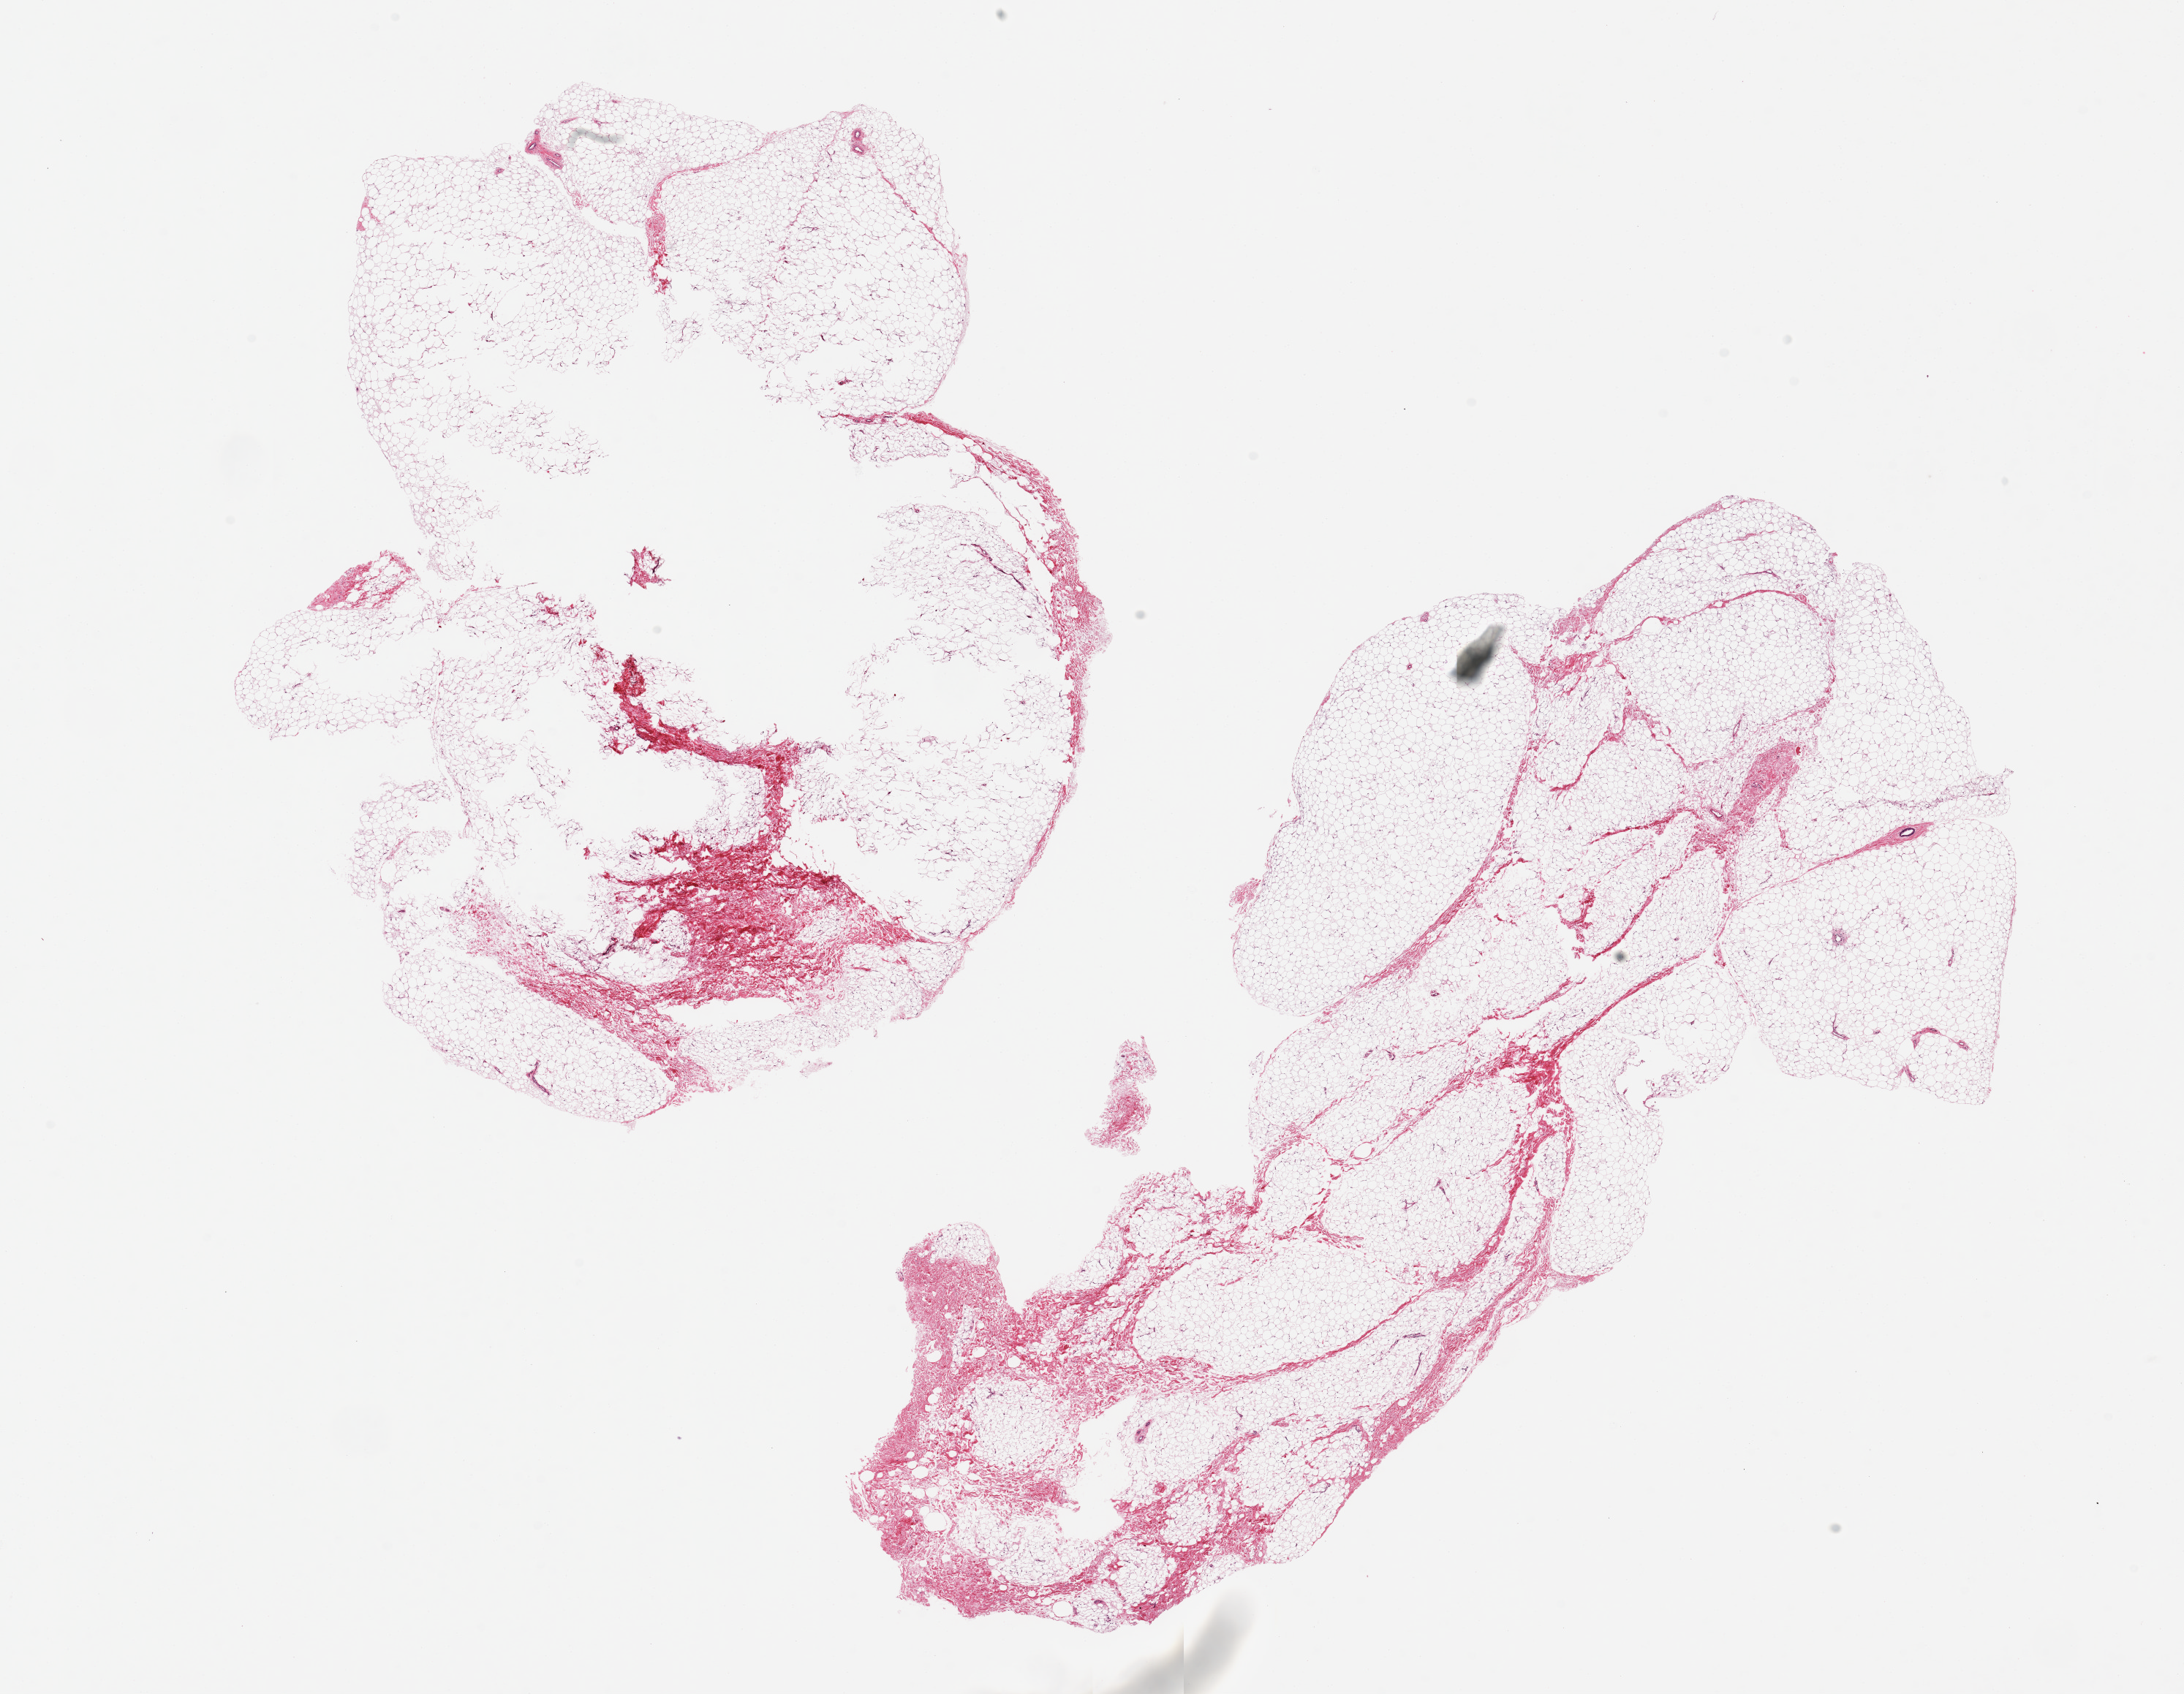
Hematoxylin and eosin (H&E) whole-slide image, low-resolution overview of the scanned area, about 23.6 x 18.3 mm (from a 20x scan), PAXgene-fixed, paraffin-embedded tissue, section of breast (target tissue), tissue donor sample.
* pathologist's review note for this sample: 2 pieces ~12x6mm. No visible ductal elements, fibro-adipose tissues only